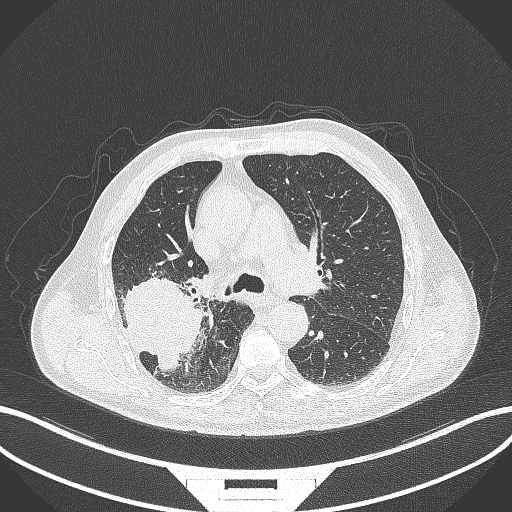
Chest CT, one axial slice; slice 262 of 429 in the series (ordered by position); reconstruction kernel B70f; 120 kVp; lung window (W 1500 / L -600 HU); 1 mm slice thickness; 512 × 512 image matrix. Patient: male, 72 years. Case-level facts recorded for this patient, not image findings: clinical TNM (as recorded): T3 N2 M0.
Structures marked on this image (bounding box drawn by a radiologist):
- lung tumour (recorded histology: adenocarcinoma): bounding box [x1, y1, x2, y2] px = [118, 273, 206, 376]